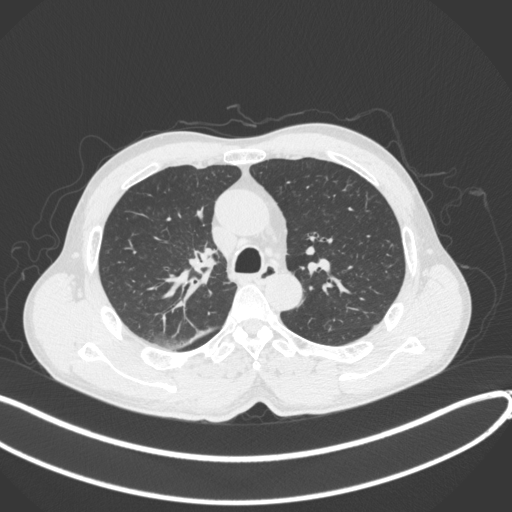
Chest CT, one axial slice. Position 267 of 409 along the scan axis. Reconstruction kernel B31f. Lung window (W 1500 / L -600 HU). 1 mm slice thickness. 512 × 512 image matrix, field of view 400 × 400 mm. Male patient, age 53 years. From the clinical record (not read from this slice): clinical TNM (as recorded): T1b N0 M0.
Outlined on this slice (bounding box drawn by a radiologist):
- lung tumour (recorded histology: squamous cell carcinoma): bounding box (x1, y1, x2, y2) in pixels: (185, 242, 221, 278)